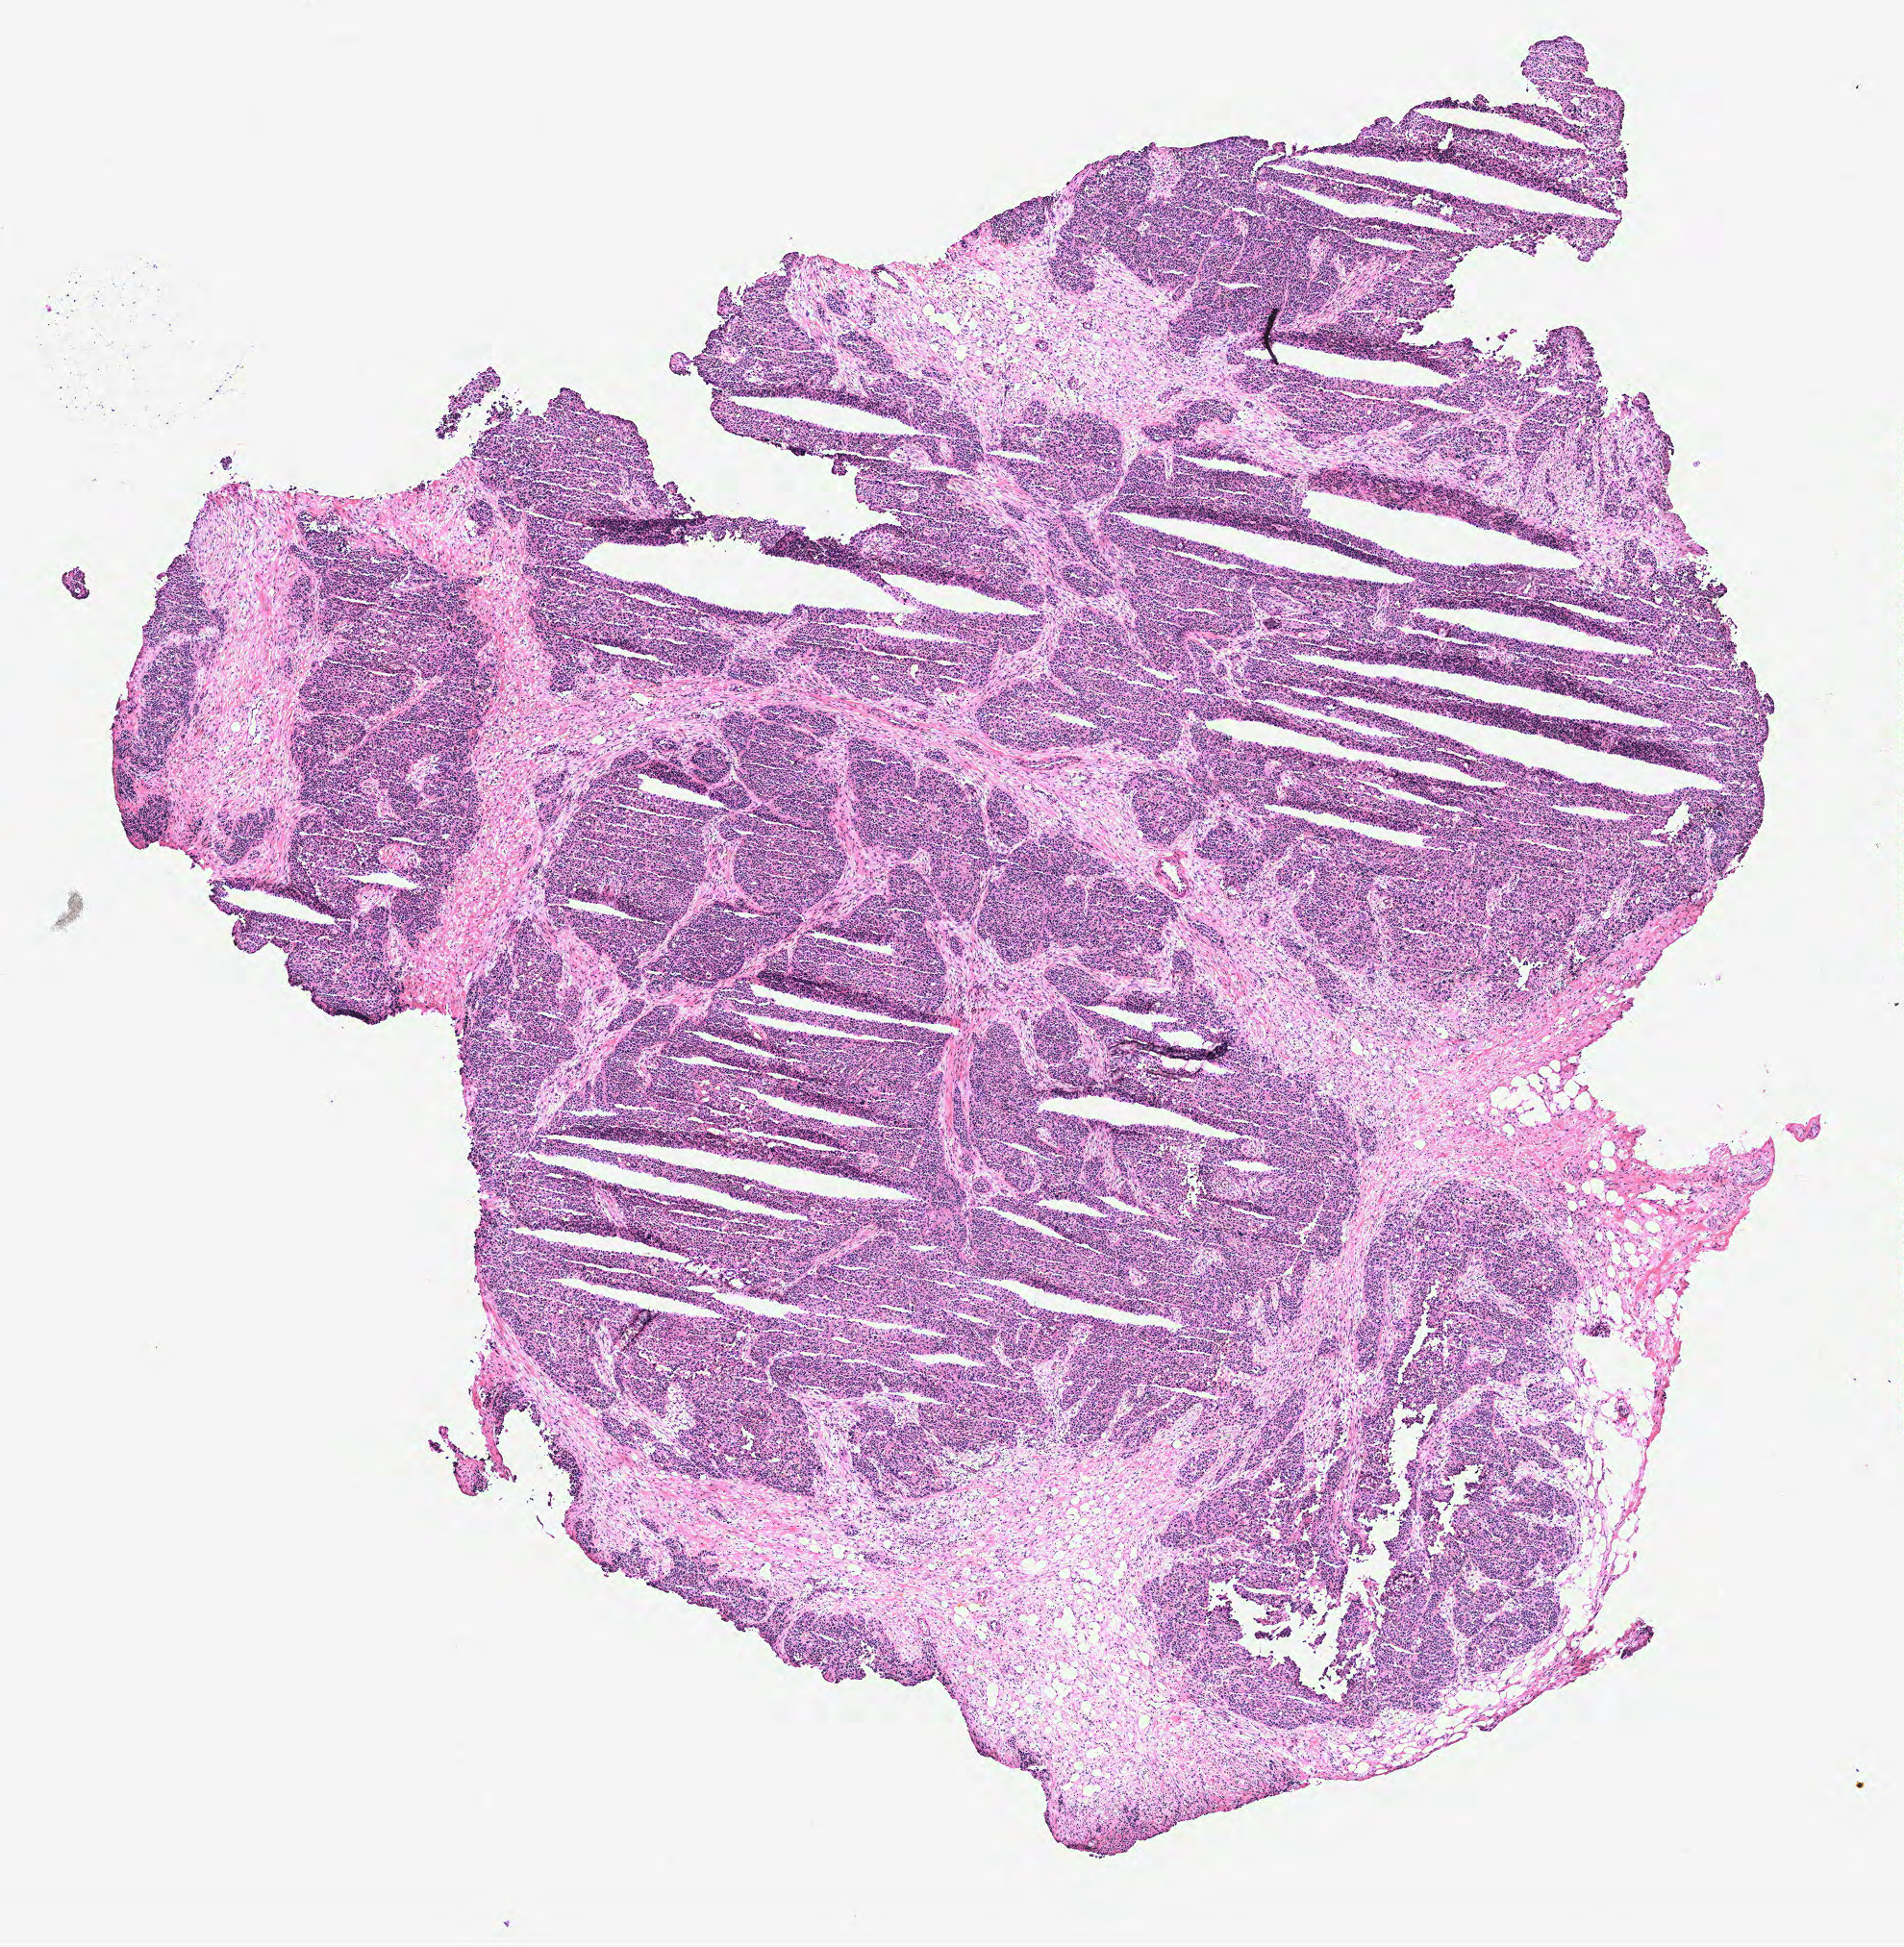
Whole-slide histology image, H&E, a low-resolution overview of the entire scanned area, about 7.9 x 8.1 mm (slide scanned at 40x), ovary, tissue type not recorded. Female patient.
Patient diagnosis: Serous adenocarcinoma, NOS (peritoneum, NOS).